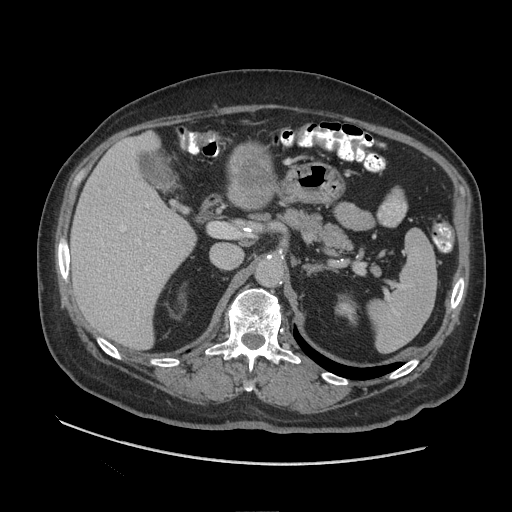
Contrast-enhanced abdominal CT (liver protocol), one axial slice. Slice 52 of 109 in the series (ordered by position). Reconstruction kernel STANDARD. 140 kVp. Soft-tissue window (W 400 / L 40 HU). 2.5 mm slice thickness. 512 × 512 image matrix, field of view 420 × 420 mm. Case-level facts recorded for this patient, not image findings: diagnosis: hepatocellular carcinoma (patient treated with transarterial chemoembolisation; whether this scan precedes or follows treatment is not stated here); TNM stage (as recorded): Stage-I; Child-Pugh class: A; tumour nodularity: uninodular.
Outlined on this slice (semi-automatic segmentation, software-assisted and operator-edited):
- liver parenchyma outside the tumour (the mass and vessels are separate outlines, so this box may not span the whole liver): bounding box (x1, y1, x2, y2) in pixels: (70, 132, 196, 348)
- mass: (231, 151, 275, 203)
- liver vessels: (98, 204, 165, 280)